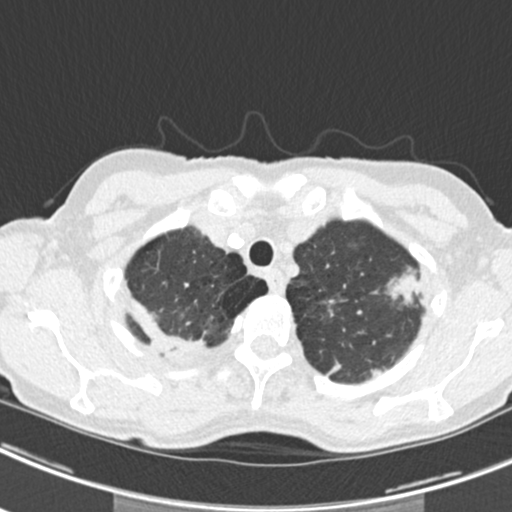
Axial slice from a low-dose chest CT screening exam; second annual screen; lung window (W 1500 / L -600 HU); 2 mm slice thickness; slice 34 of 219 in the series; 512 × 512 image matrix, field of view 298 × 298 mm. Female participant, aged 63 years at enrolment. Current smoker at enrolment.
• Lesion marked by an expert reader, bounding box (x1, y1, x2, y2) in pixels: (368, 256, 431, 316).
• The screening reader recorded 9 non-calcified nodules or masses ≥4 mm on this exam (left upper lobe, right upper lobe, left upper lobe, left lower lobe, right middle lobe, left lower lobe, left lower lobe, right lower lobe, right lower lobe); which of them this box marks is not recorded.
• Later outcome: lung cancer diagnosed 408 days after this screen (after the third annual screen) — bronchiolo-alveolar adenocarcinoma, NOS, right upper lobe, right middle lobe, right lower lobe, left upper lobe, left lower lobe, moderately differentiated (G2), stage IV (AJCC 6th edition).